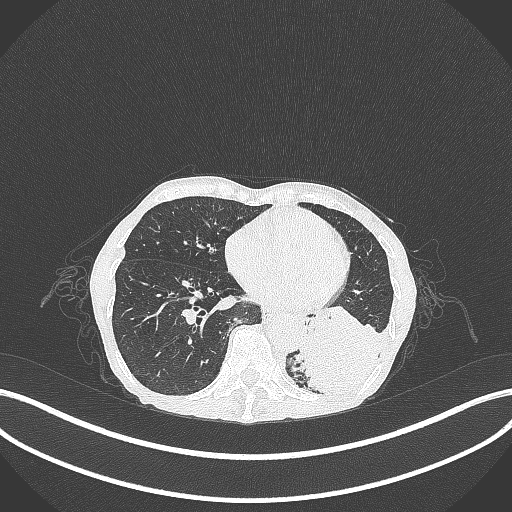
Chest CT, one axial slice; position 89 of 347 along the scan axis; reconstruction kernel B70f; 120 kVp; lung window (W 1500 / L -600 HU); 1 mm slice thickness; 512 × 512 image matrix, field of view 400 × 400 mm. Patient: female, 70 years. Case-level facts recorded for this patient, not image findings: clinical TNM (as recorded): T3 N0 M0.
Outlined on this slice (bounding box drawn by a radiologist):
- lung tumour (recorded histology: small cell carcinoma): bounding box <293,313,384,398> (left, top, right, bottom; pixels)